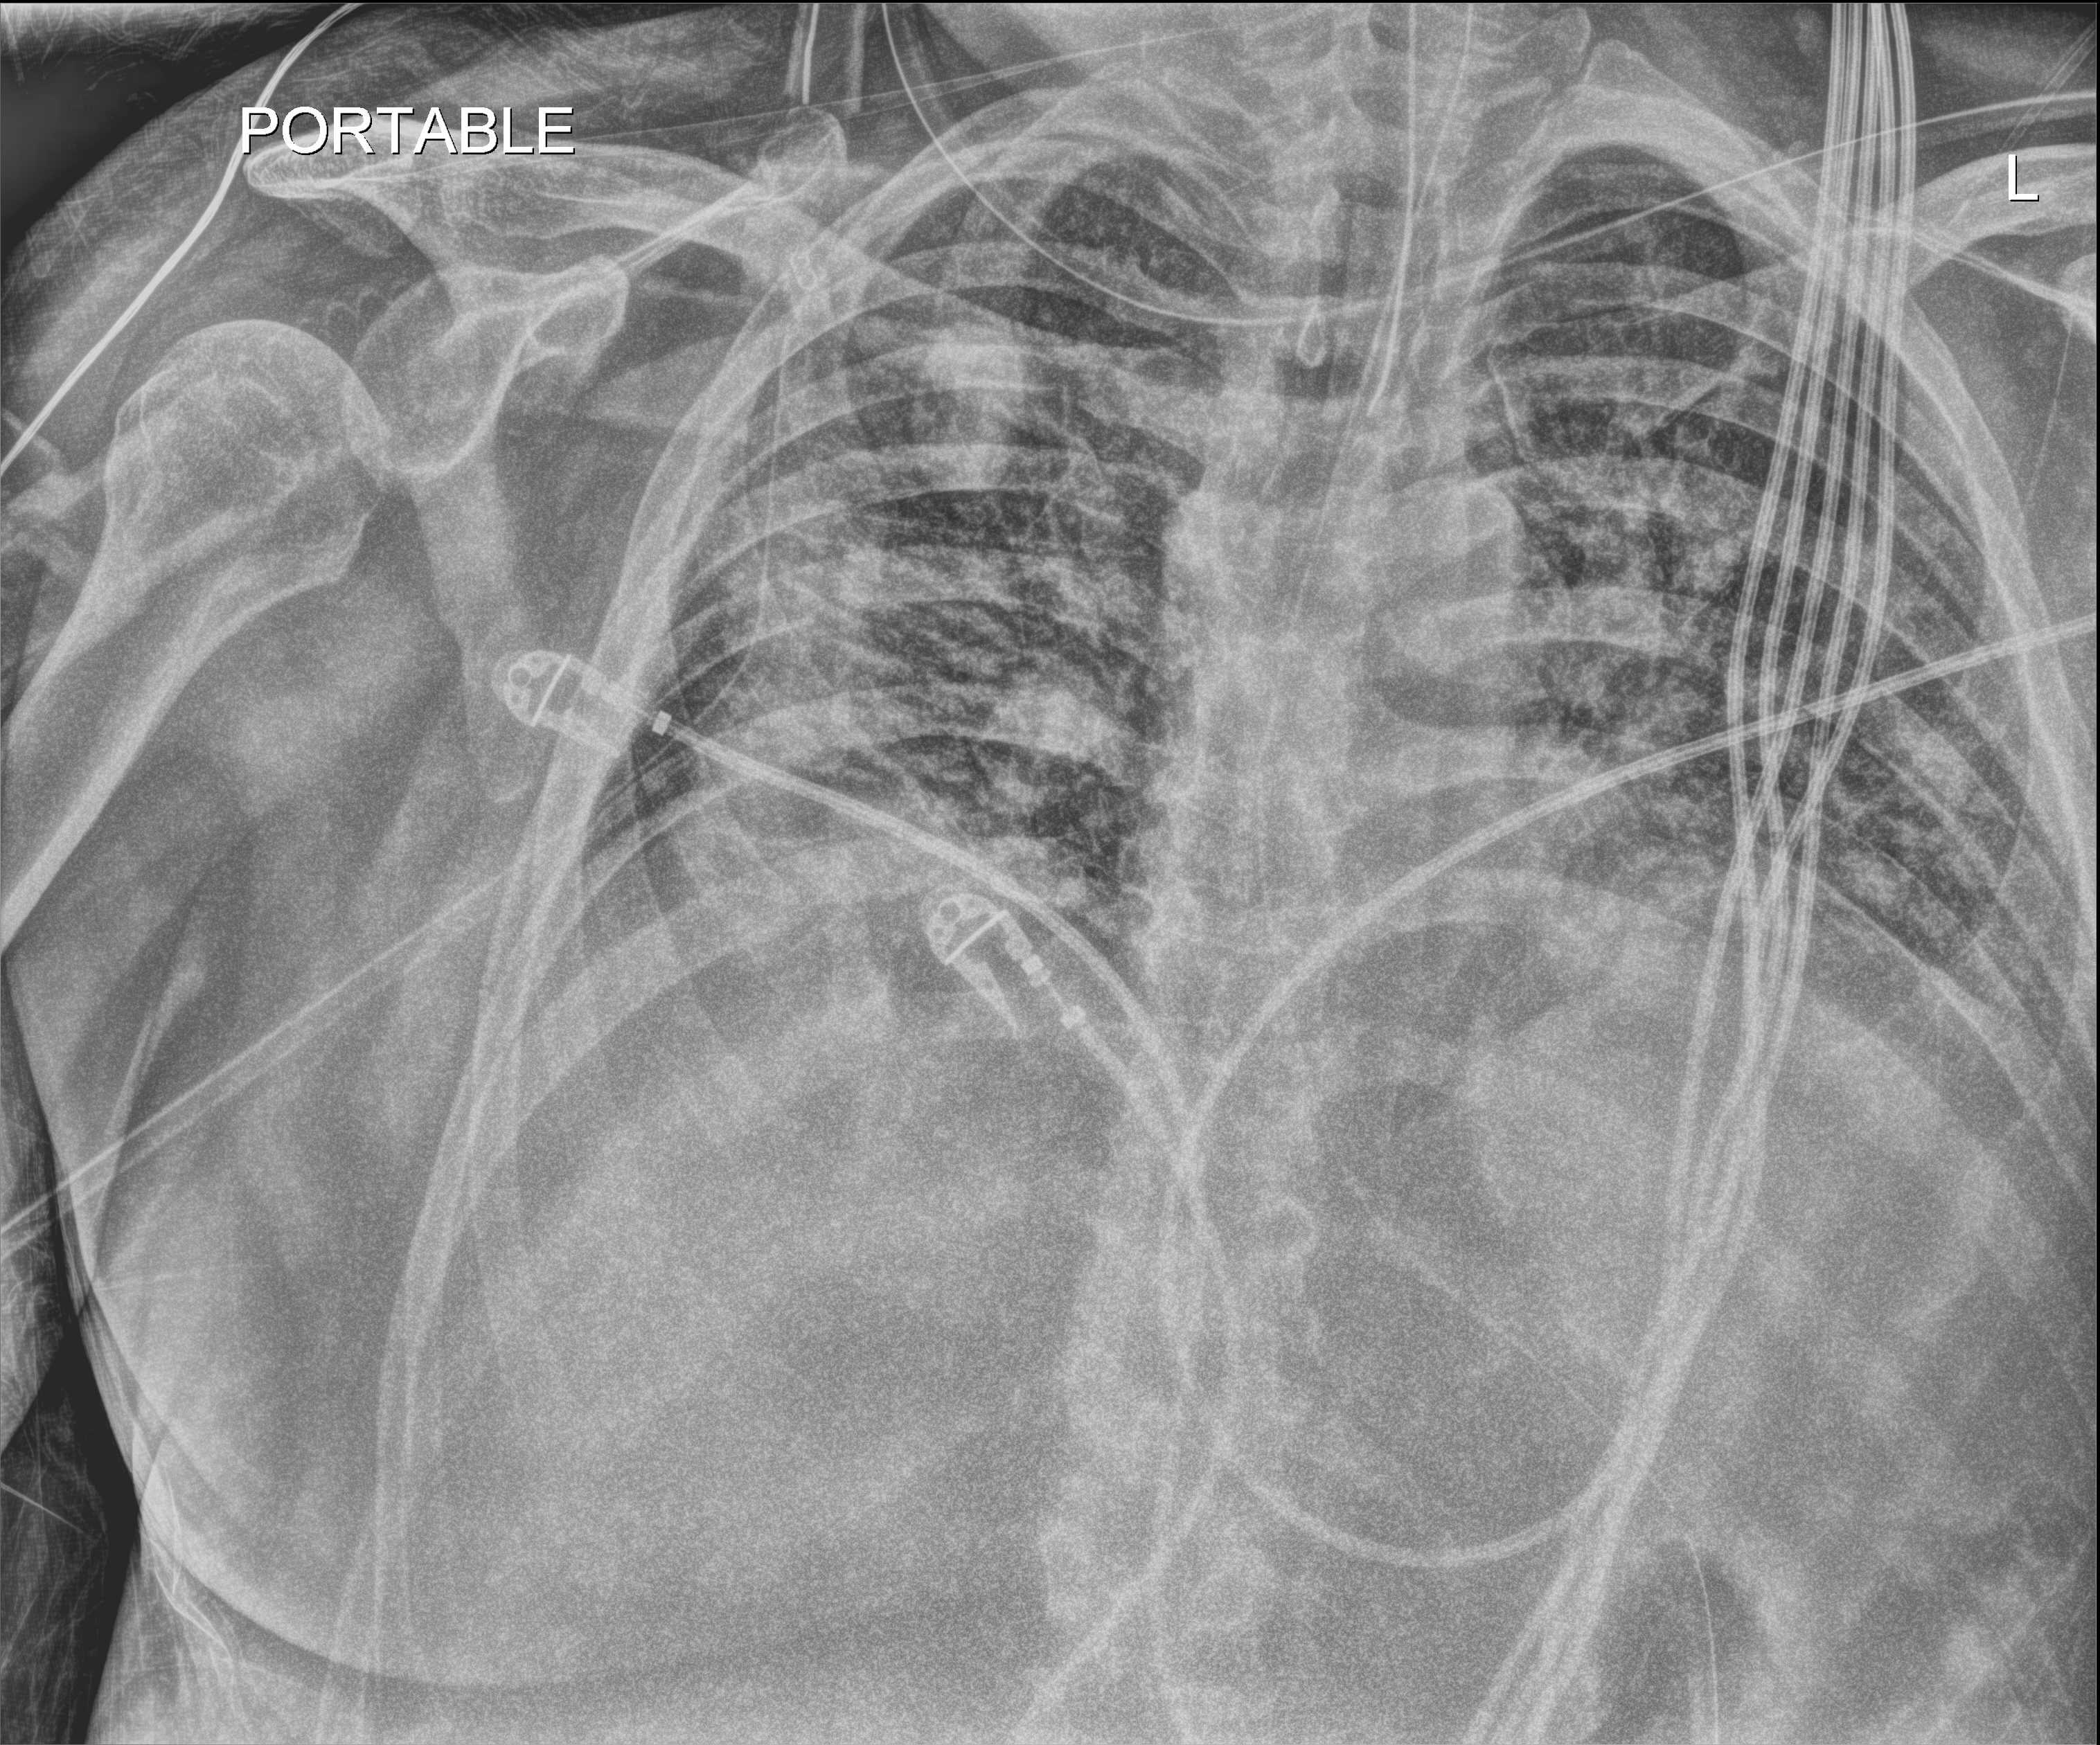
Chest X-ray (portable), anteroposterior (AP) projection. Female patient hospitalised with COVID-19, age 60–74 years.
Hospital-stay facts (about this admission, not read from this image; timing relative to this image not recorded):
- other chronic lung disease (admission record): no
- admitted to intensive care during this hospital stay: yes
- mechanically ventilated during this hospital stay: yes